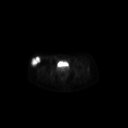
FDG PET of an extremity soft-tissue mass (from a PET/CT study), one axial slice. Position 64 of 267 along the scan axis. 128 × 128 image matrix, field of view 700 × 700 mm. Female patient, age 34 years. Case-level facts recorded for this patient, not image findings: histological type: synovial sarcoma; grade: intermediate; site of the primary tumour: right thigh.
Annotated regions visible in this slice (expert contour drawn on MRI and transferred to this co-registered scan by the dataset authors):
- gross tumour volume including surrounding oedema: bounding box <30,56,40,67> (left, top, right, bottom; pixels)
- gross tumour volume (mass): <30,56,41,67>